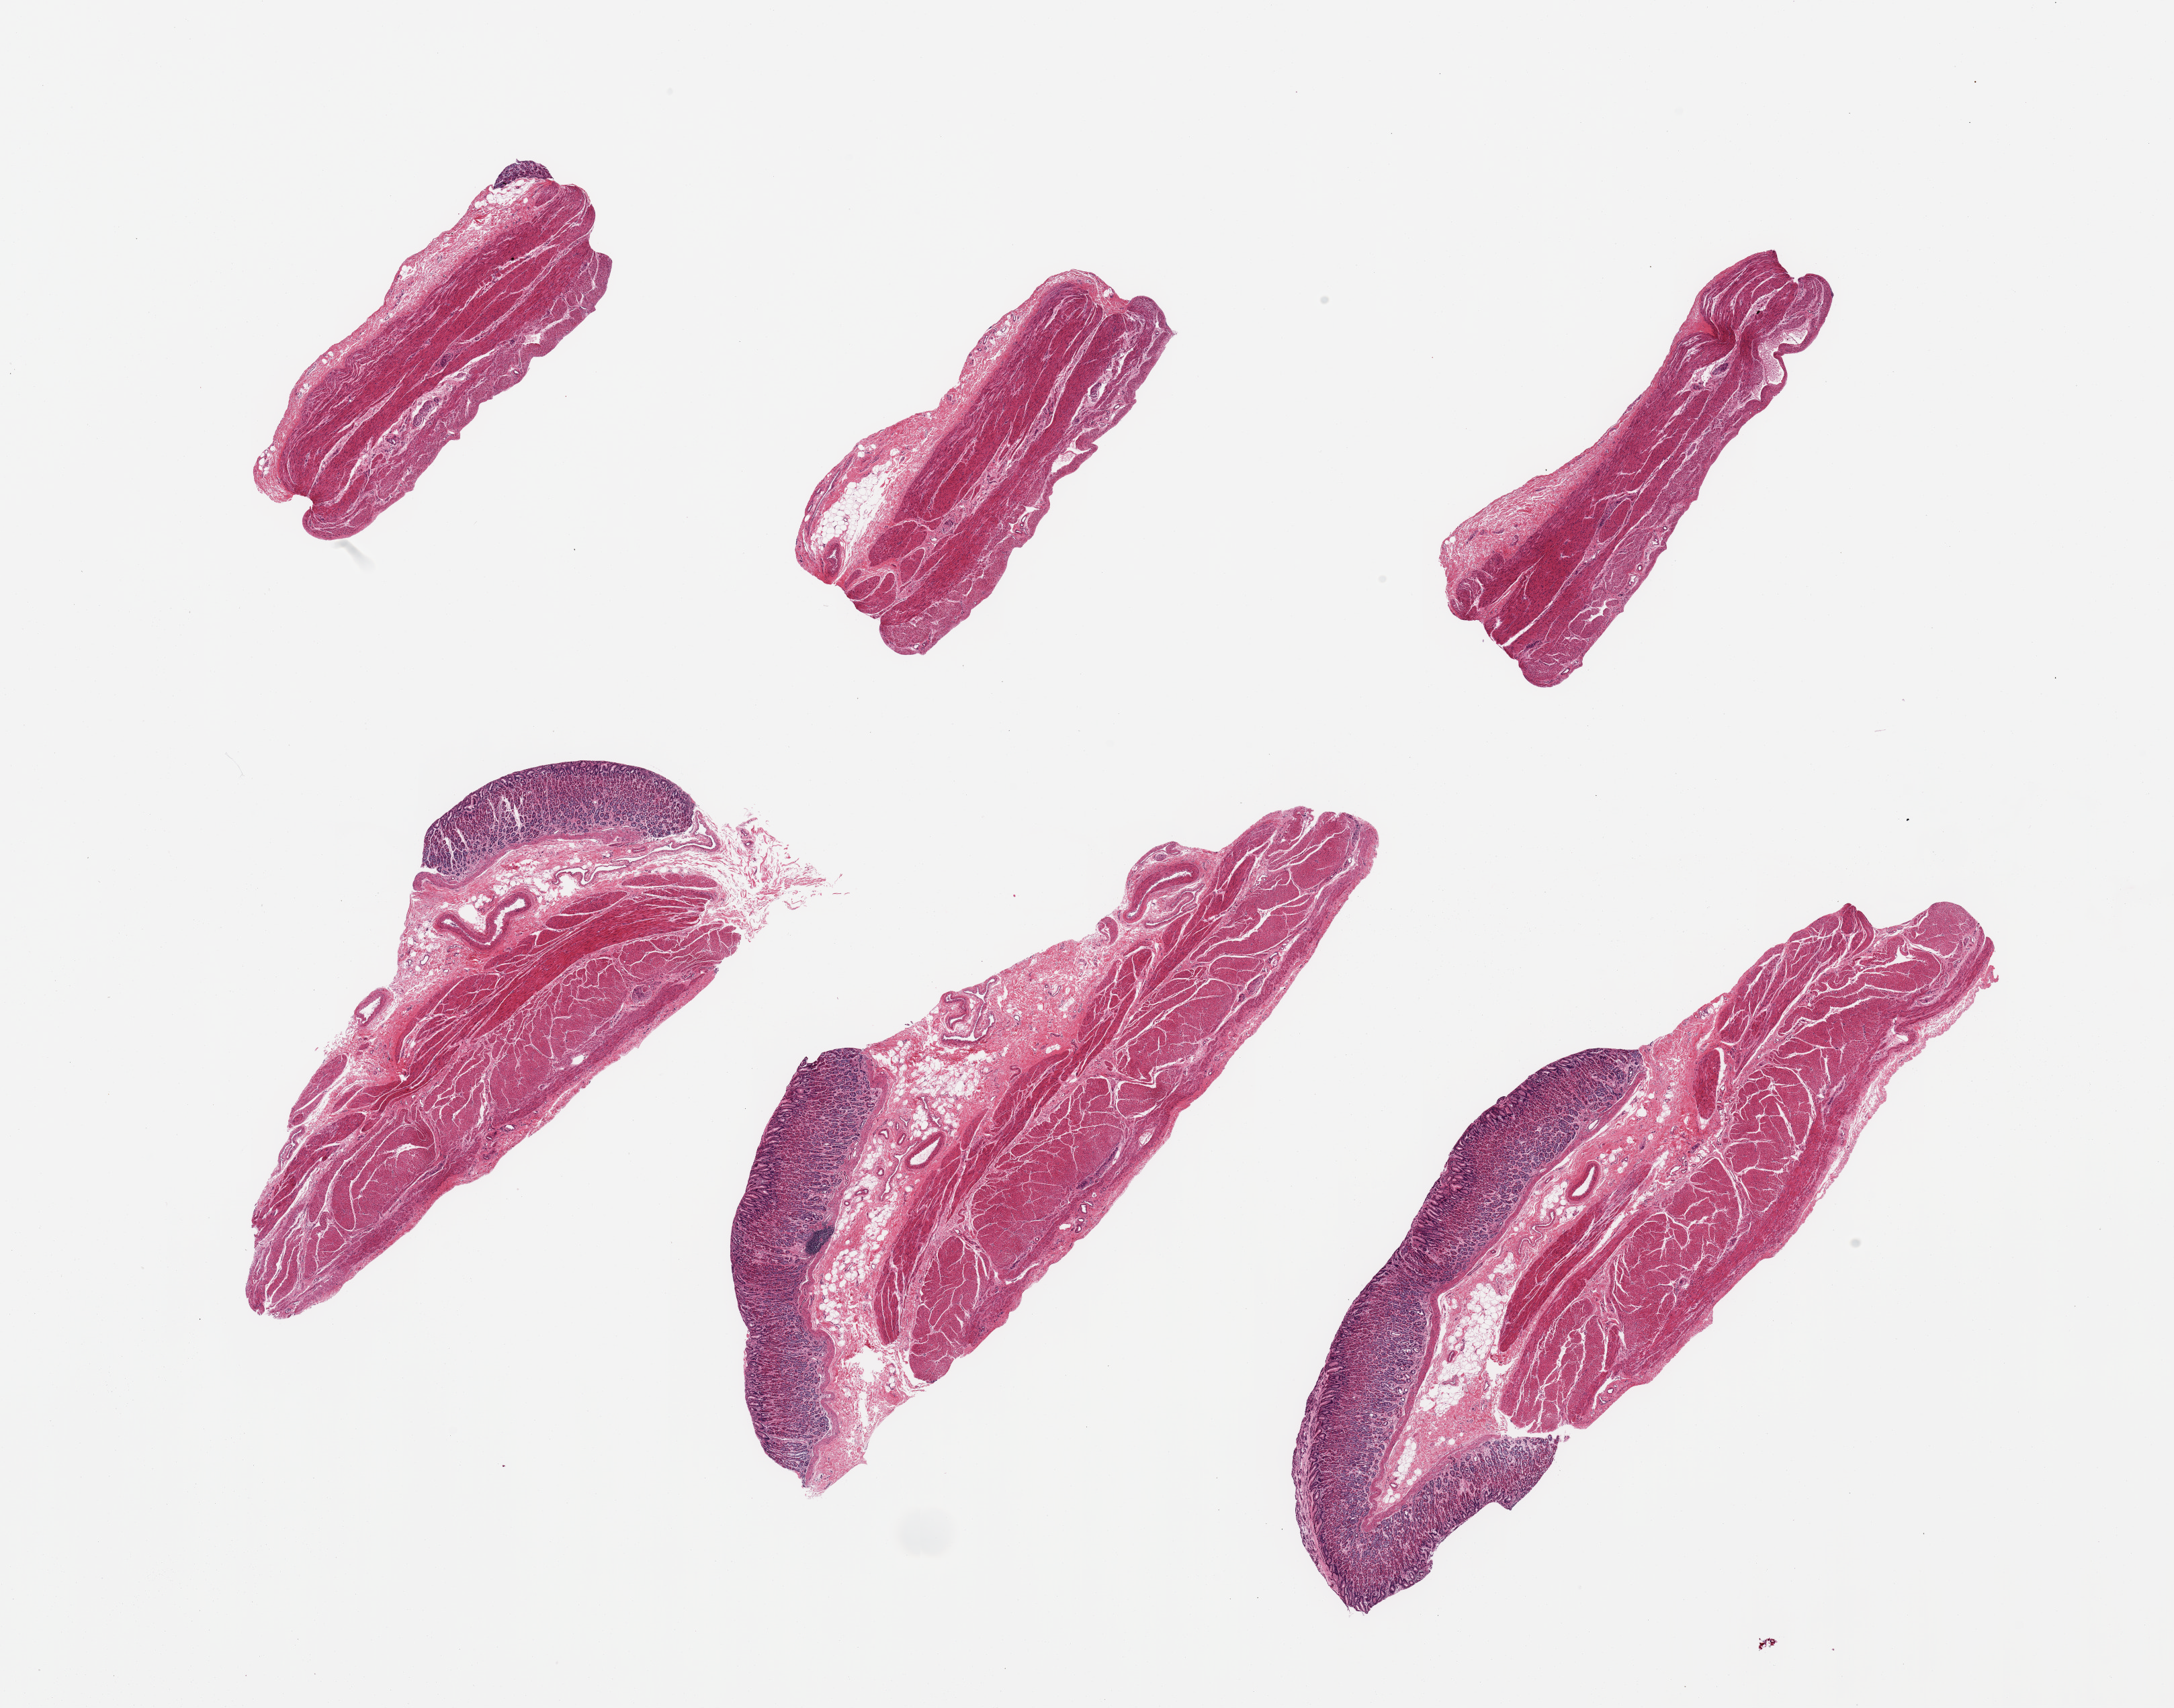
Digitized hematoxylin and eosin (H&E)-stained section — whole scanned area (about 25.6 x 20.1 mm) shown as a low-resolution overview; PAXgene-fixed, paraffin-embedded tissue; sampled site (target tissue): stomach; tissue donor sample. Donor sex: male.
• pathologist's review note for this sample: 6 pieces; two pieces devoid of gastric mucosa; well preserved muscularis